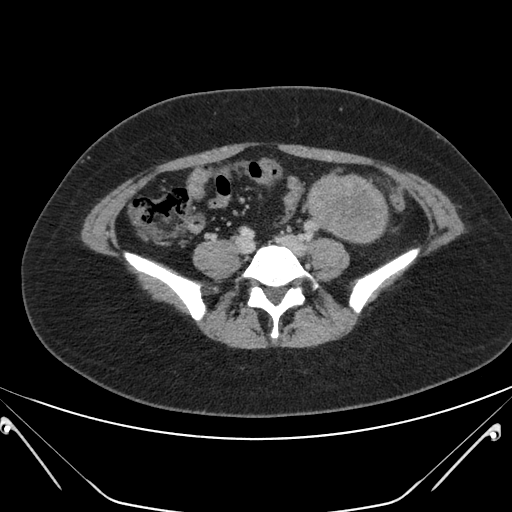
Contrast-enhanced abdominal CT, one axial slice. Slice 67 of 168 in the series (ordered by position). 120 kVp. Intravenous contrast given. Soft-tissue window (W 400 / L 40 HU). 3 mm slice thickness. 512 × 512 image matrix, field of view 394 × 394 mm. Female patient, age 26 years. From the clinical record (not read from this slice): diagnosis: adrenocortical carcinoma; tumour side: left adrenal; tumour size at pathology: 28 cm.
Annotated regions visible in this slice (semi-automatic segmentation, software-assisted and operator-edited):
- mass: bounding box [x1, y1, x2, y2] px = [310, 178, 384, 240]